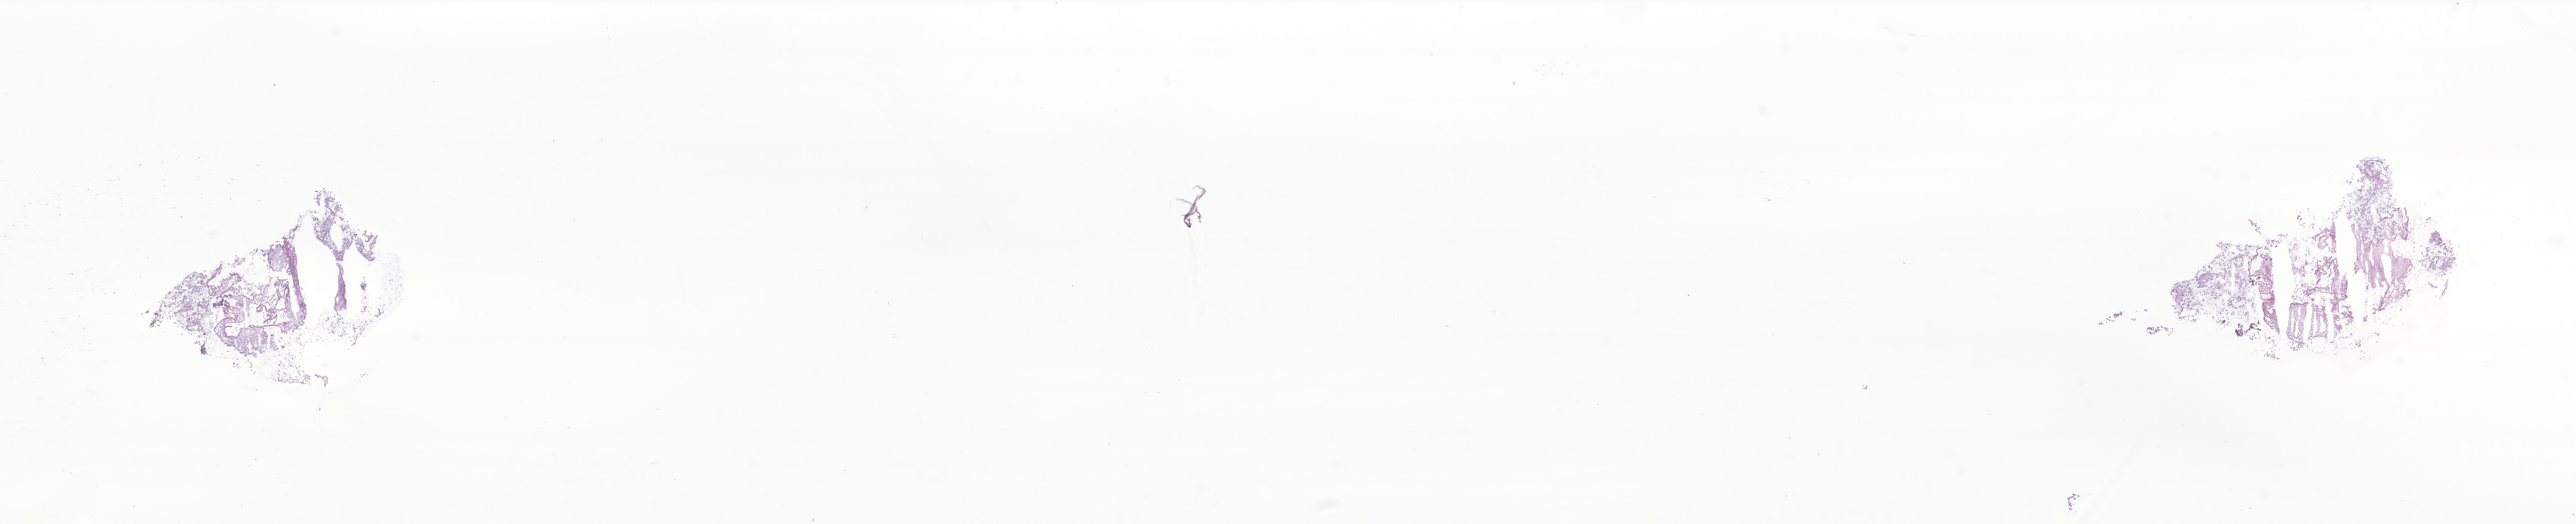
Whole-slide image, H&E stain of tumor tissue from the brain — low-resolution overview of the scanned area, about 28.7 x 5.8 mm, frozen section (OCT-embedded). Patient male; age 75 months.
- diagnosis: Astrocytoma, NOS